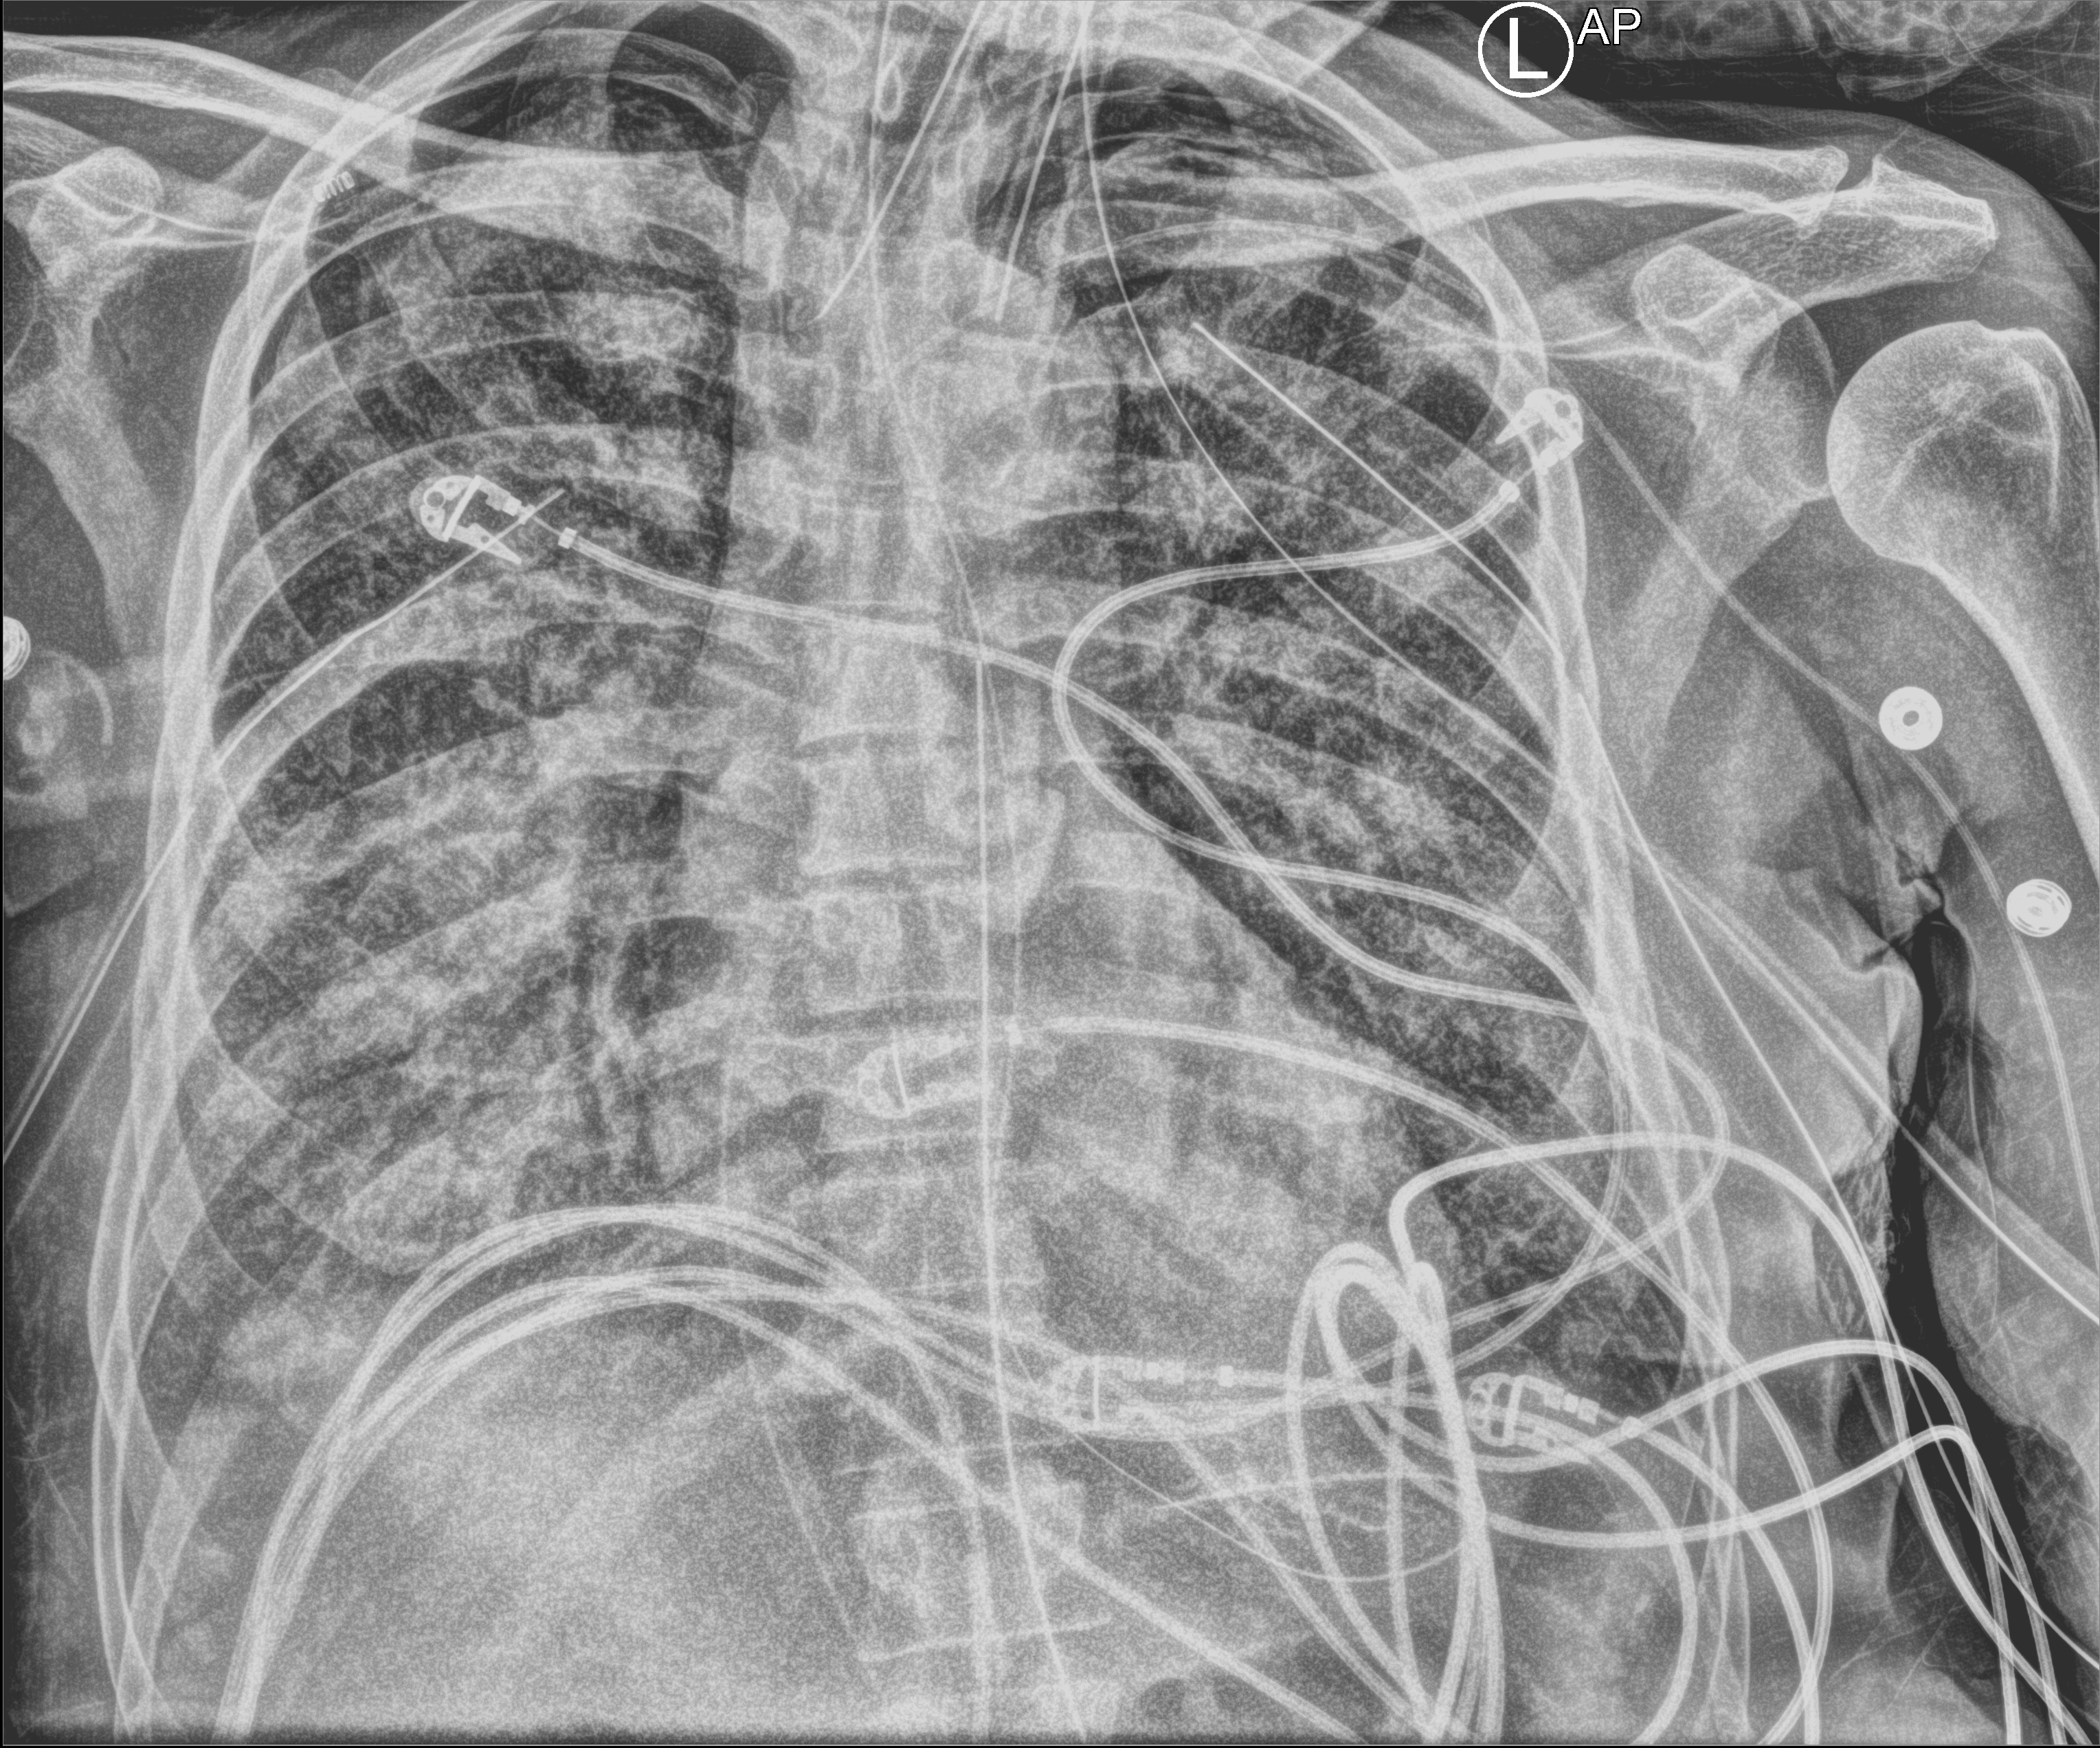
Bedside chest radiograph (computed radiography); anteroposterior (AP) projection. Patient hospitalised with COVID-19; male, aged 60–74 years.
Hospital-stay facts (about this admission, not read from this image; timing relative to this image not recorded): smoking status (admission record): former; admitted to intensive care during this hospital stay: yes; mechanically ventilated during this hospital stay: yes.